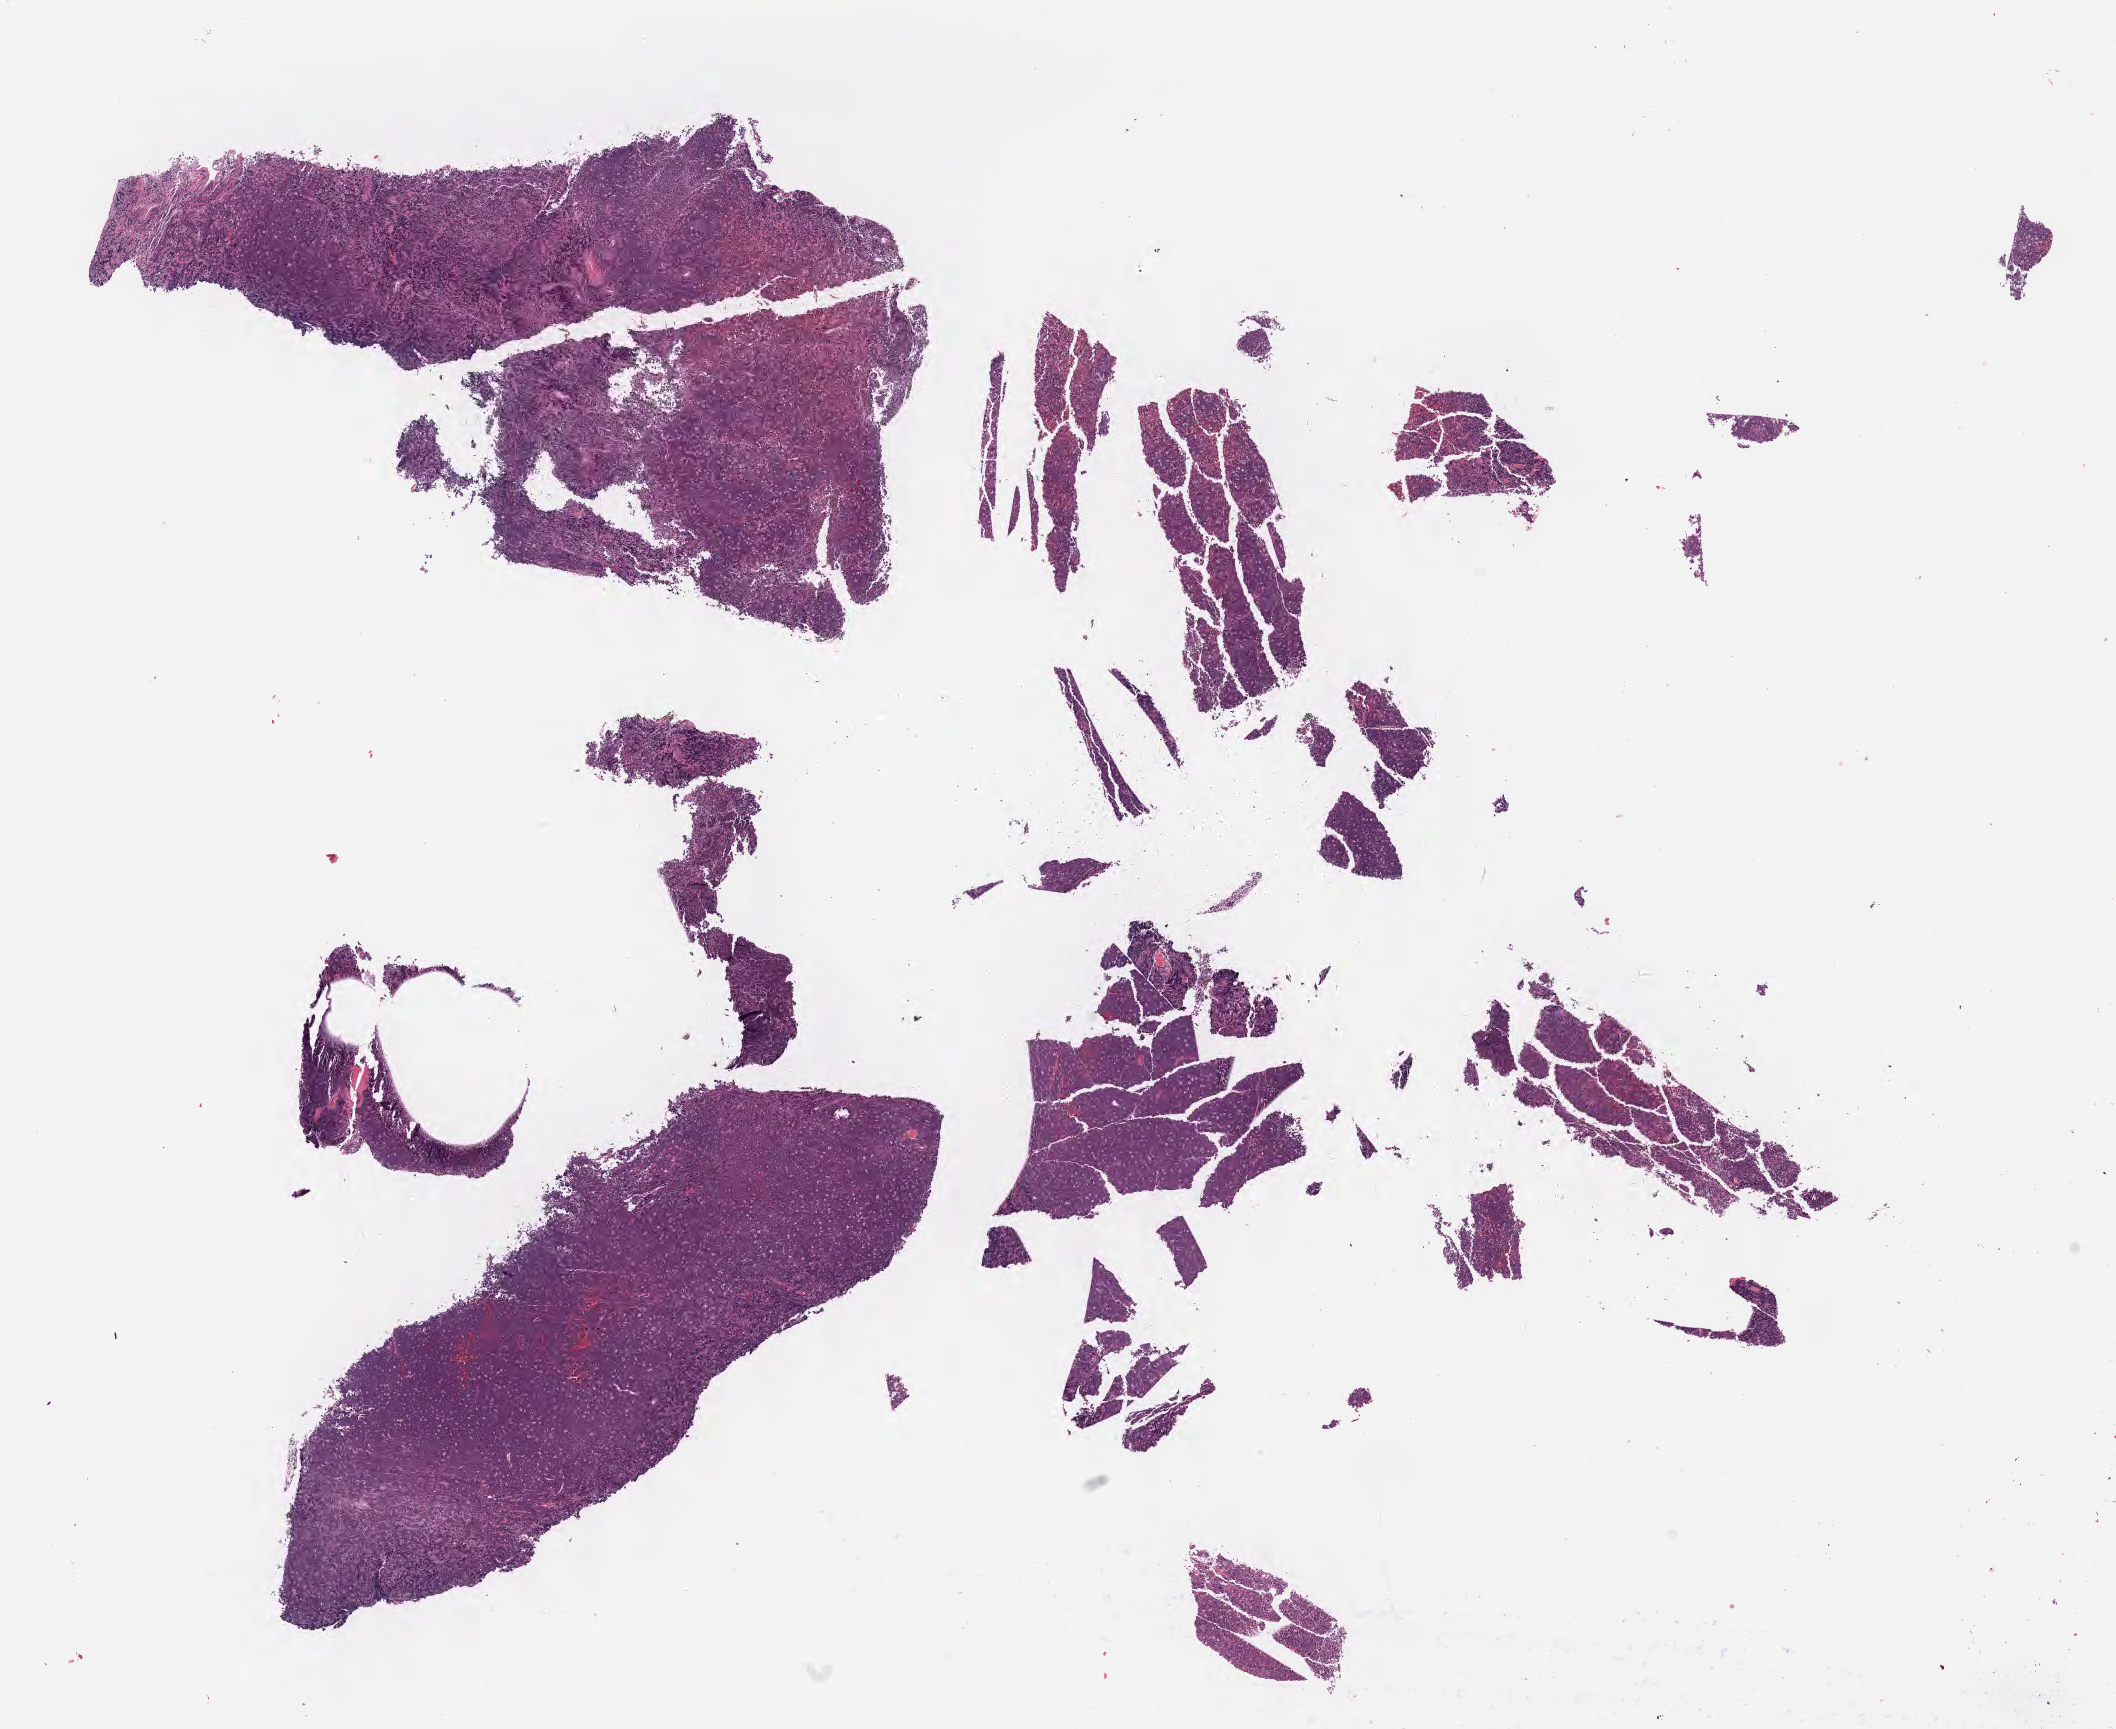
Hematoxylin and eosin (H&E) whole-slide image, shown as a low-resolution overview of the whole scanned area (about 17.1 x 14.0 mm), specimen: tumor tissue. Patient: male, age at initial diagnosis 9 years.
Diagnosis: Burkitt lymphoma, NOS.